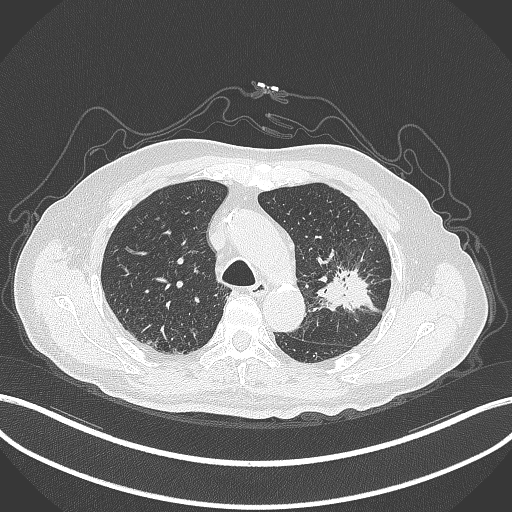
Chest CT, one axial slice. Position 209 of 331 along the scan axis. 120 kVp. Lung window (W 1500 / L -600 HU). 1 mm slice thickness. 512 × 512 image matrix, field of view 400 × 400 mm. Male patient, age 79 years. From the clinical record (not read from this slice): clinical TNM (as recorded): T2a N1 M1; histopathological grade: G3.
Structures marked on this image (rectangle marked by the reading radiologist):
- lung tumour (recorded histology: adenocarcinoma): bounding box (x1, y1, x2, y2) in pixels: (310, 261, 383, 320)